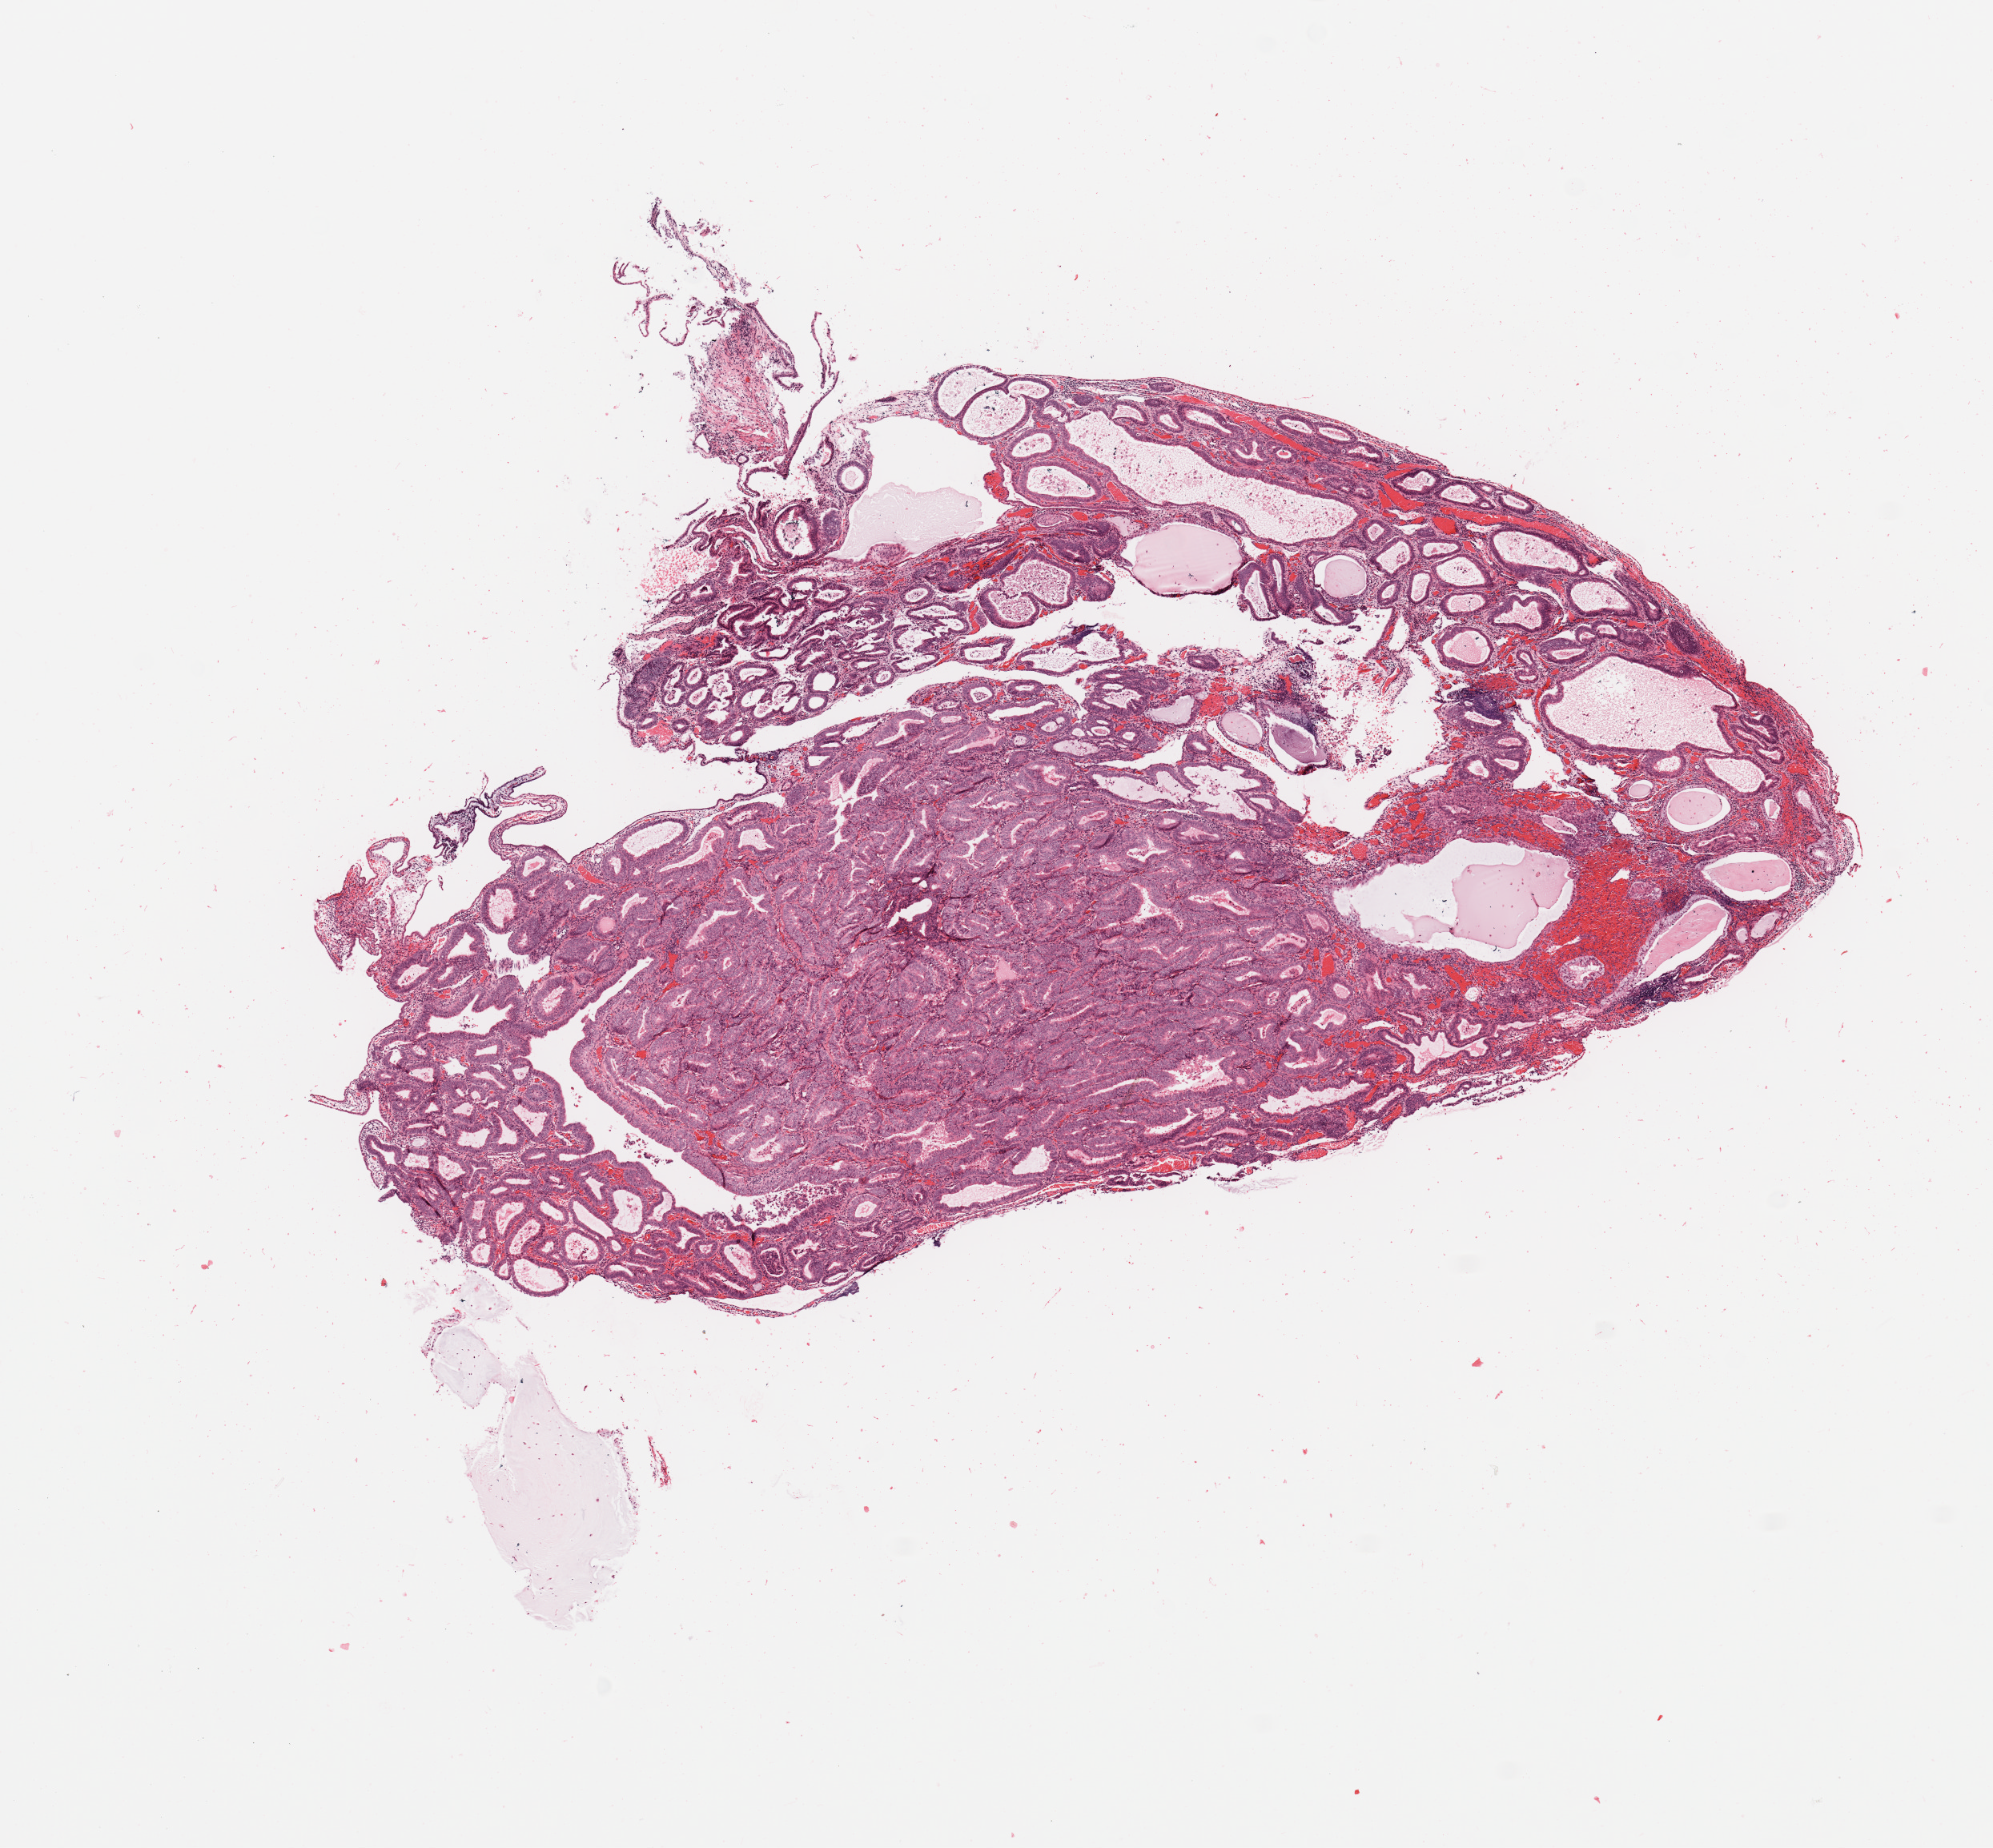
Digitized H&E tissue section (whole slide) — shown as a low-resolution overview of the whole scanned area (about 9.8 x 9.1 mm, from a 20x scan). Uterus, tumour tissue. Patient: female, age 60 years. Histologic grade: G2 (moderately differentiated).
AJCC pathologic stage: I. Histologic diagnosis: Endometrioid adenocarcinoma, NOS.